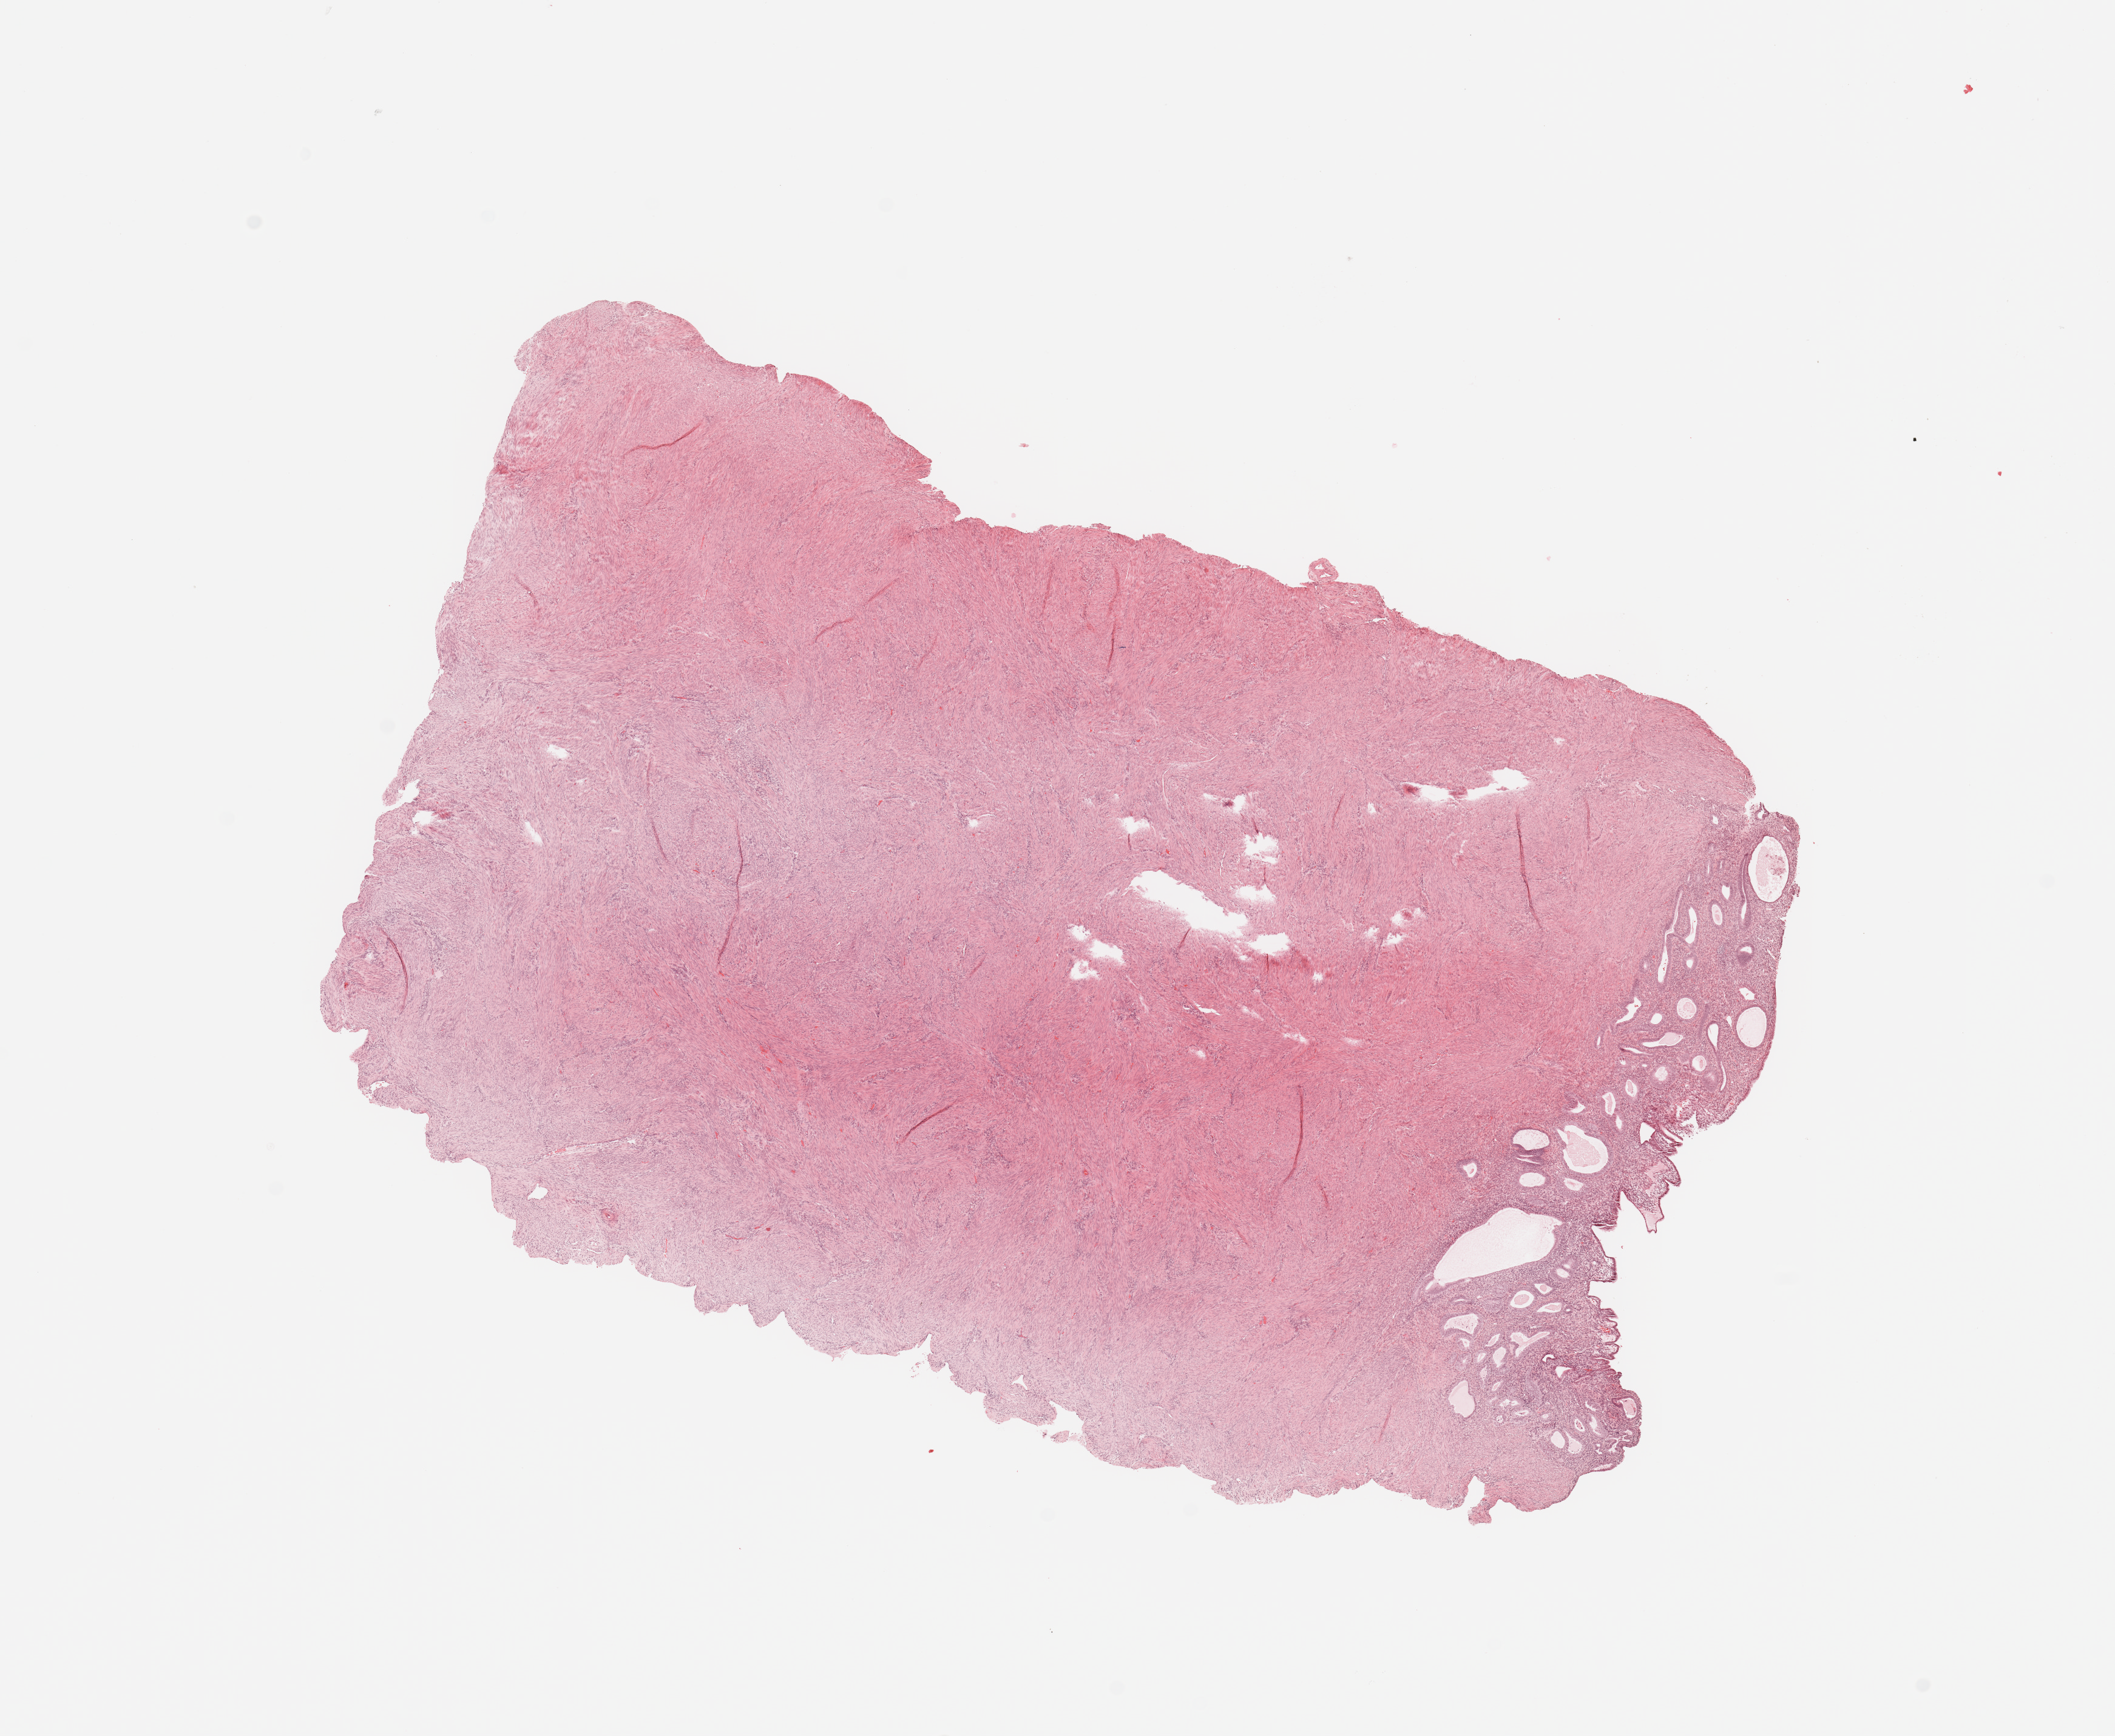
Whole-slide histology image, H&E-stained, low-resolution overview of the scanned area, about 13.8 x 11.3 mm, normal (non-tumour) tissue sample, uterus. 65-year-old female patient.
This section: normal (non-tumour) tissue from the same patient. Patient diagnosis: Endometrioid adenocarcinoma, NOS.